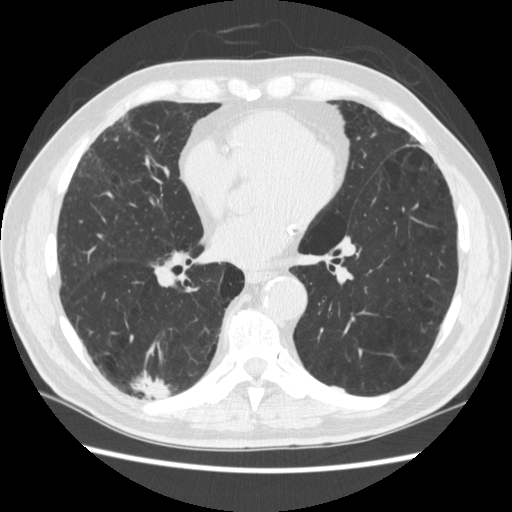
Low-dose screening chest CT, one axial slice; slice 120 of 266 in the series (ordered by position); 120 kVp; lung window (W 1500 / L -600 HU); 1.25 mm slice thickness; 512 × 512 image matrix, field of view 360 × 360 mm.
Outlined on this slice (expert manual segmentation):
- lesion 1 (tumor, upper lobe of right lung): bounding box (x1, y1, x2, y2) in pixels: (136, 374, 170, 399)